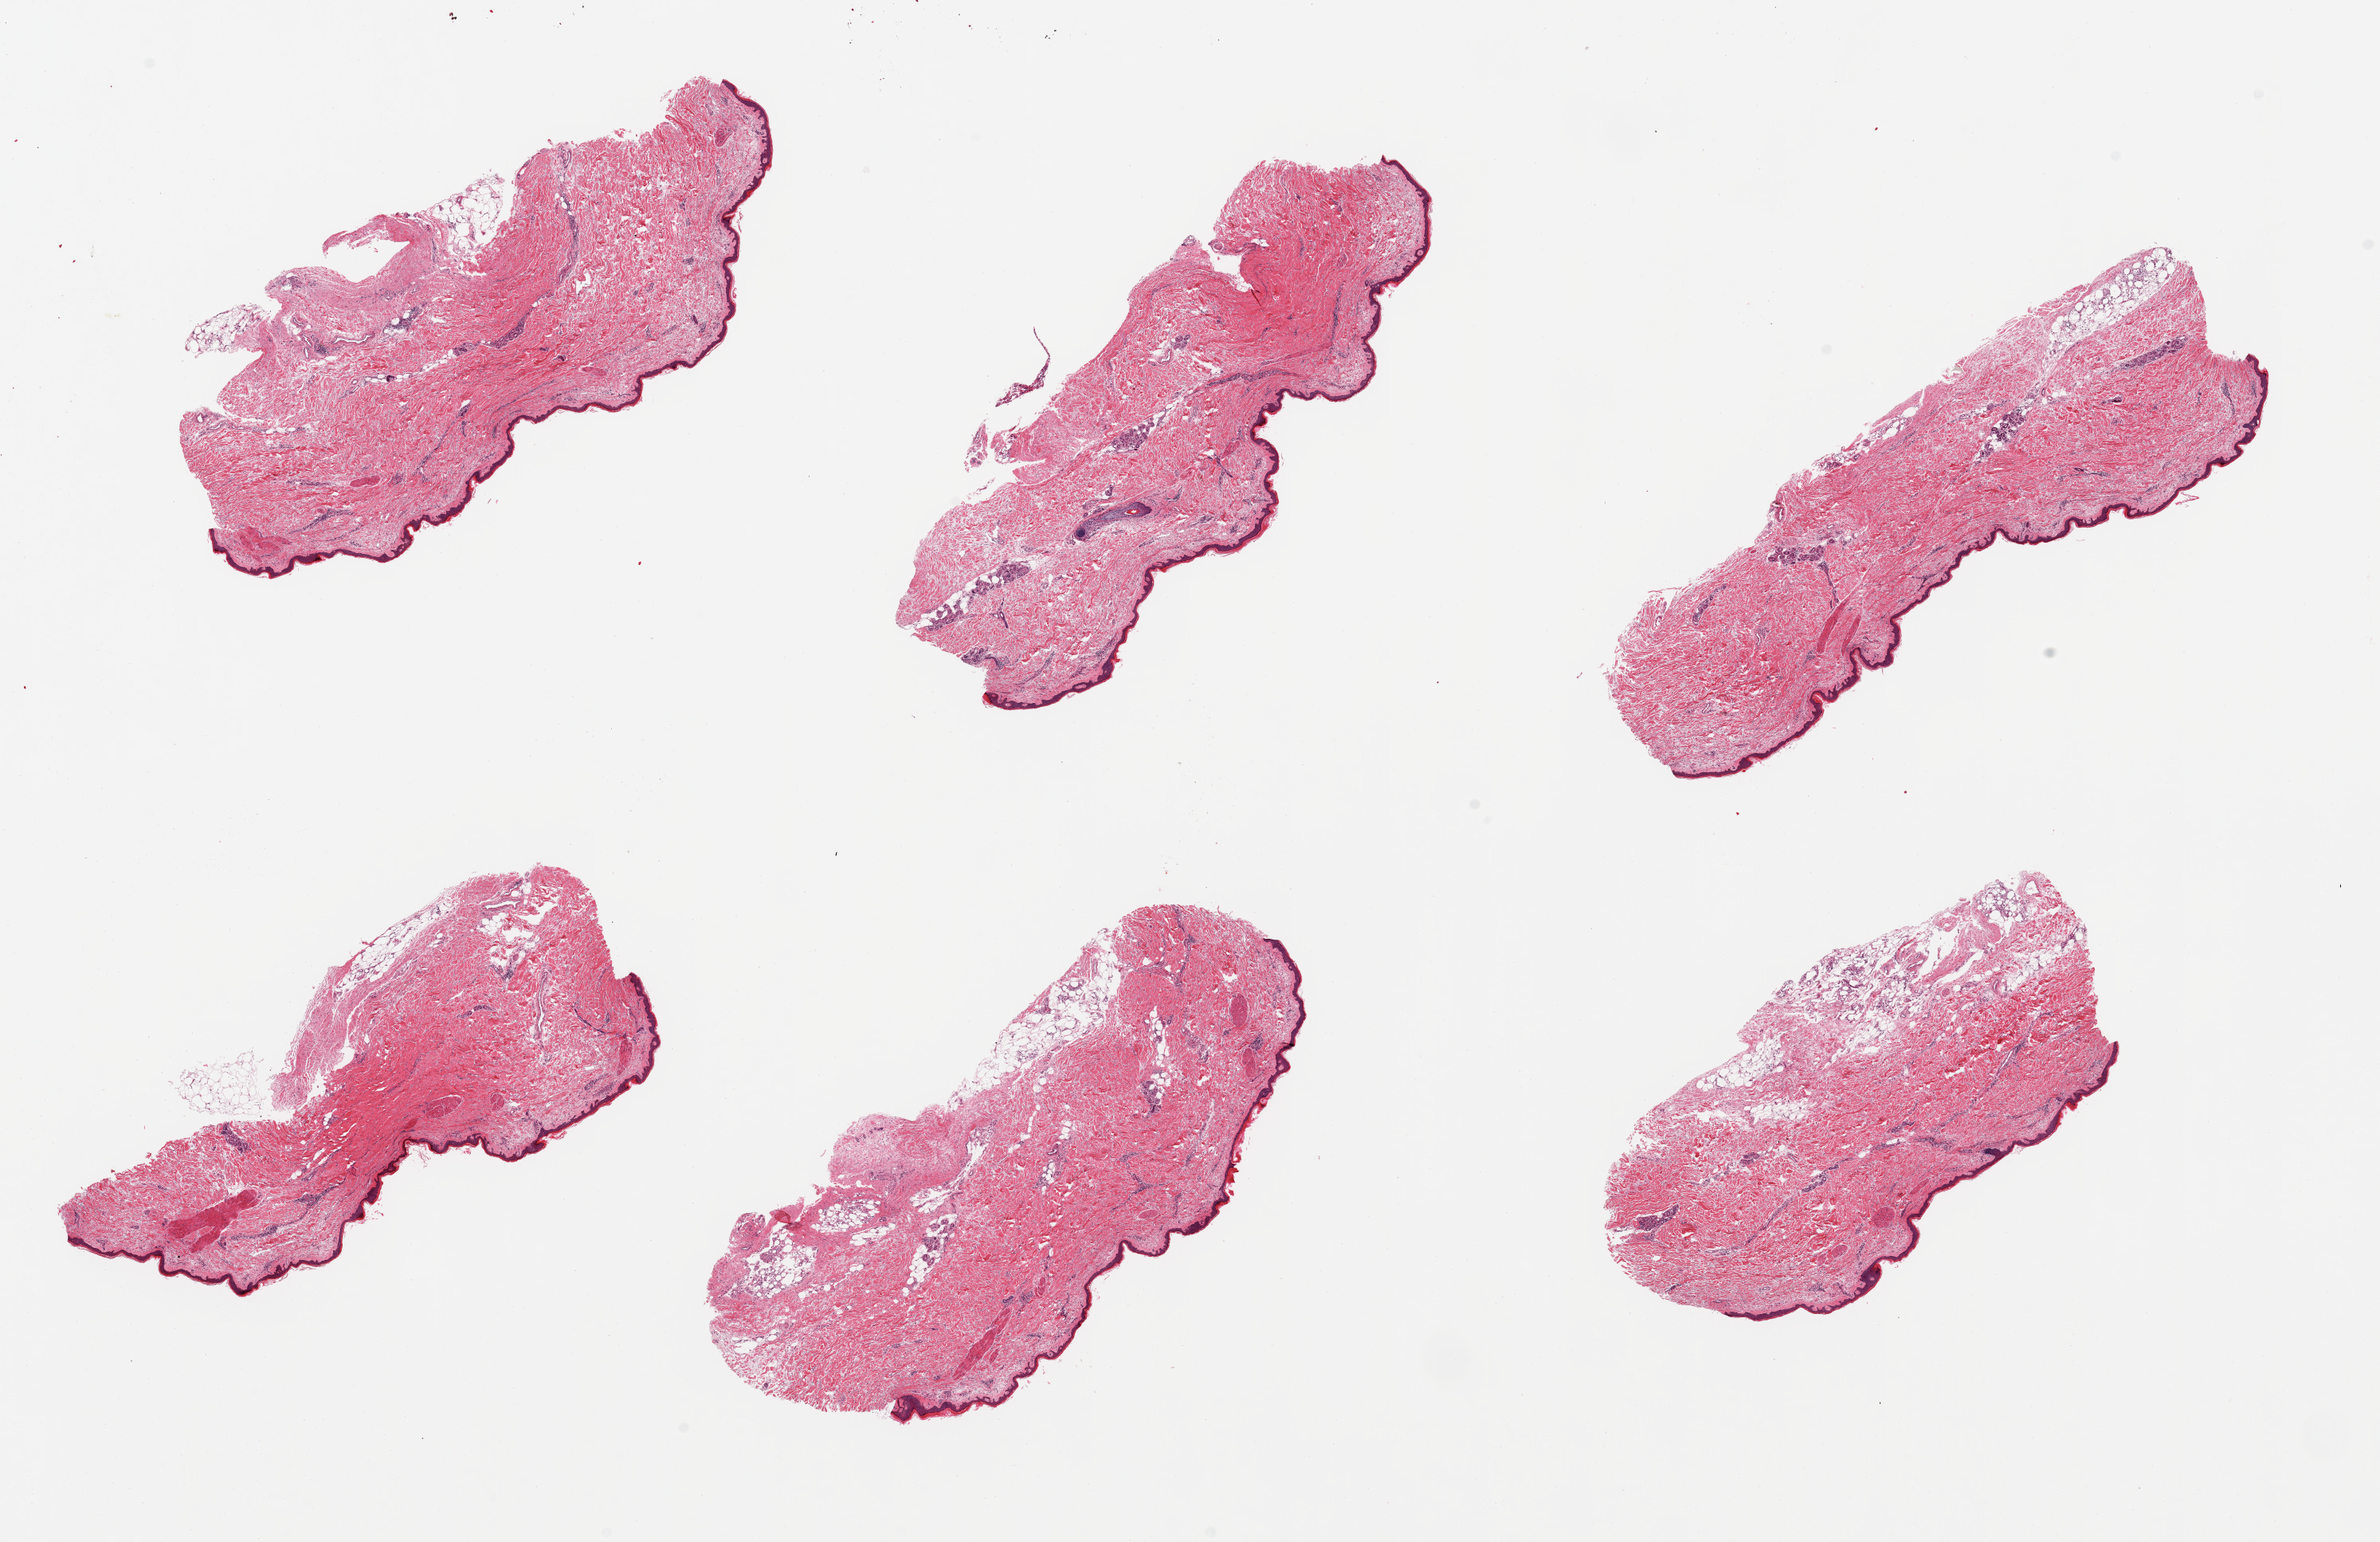
H&E whole-slide image, brightfield — shown as a low-resolution overview of the whole scanned area (about 23.6 x 15.3 mm); PAXgene-fixed, paraffin-embedded tissue; target tissue: skin of lower leg; donor tissue sample. Male donor.
Reviewer comment on this tissue sample: 6 pieces; well trimmed; up to 10% dermal fat.